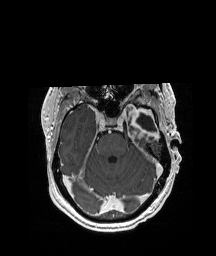
Brain MRI from a brain-tumour surgery series, one axial slice; slice 137 of 208 in the series (ordered by position); T1-weighted post-contrast; 1 mm slice thickness; 216 × 256 image matrix, field of view 228 × 270 mm. From the clinical record (not read from this slice): histopathology: Glioblastoma; WHO grade: 4; IDH mutation: no.
Annotated regions visible in this slice (expert manual segmentation):
- previous resection cavity: bounding box (x1, y1, x2, y2) in pixels: (136, 113, 157, 132)
- tumour: (123, 100, 158, 134)